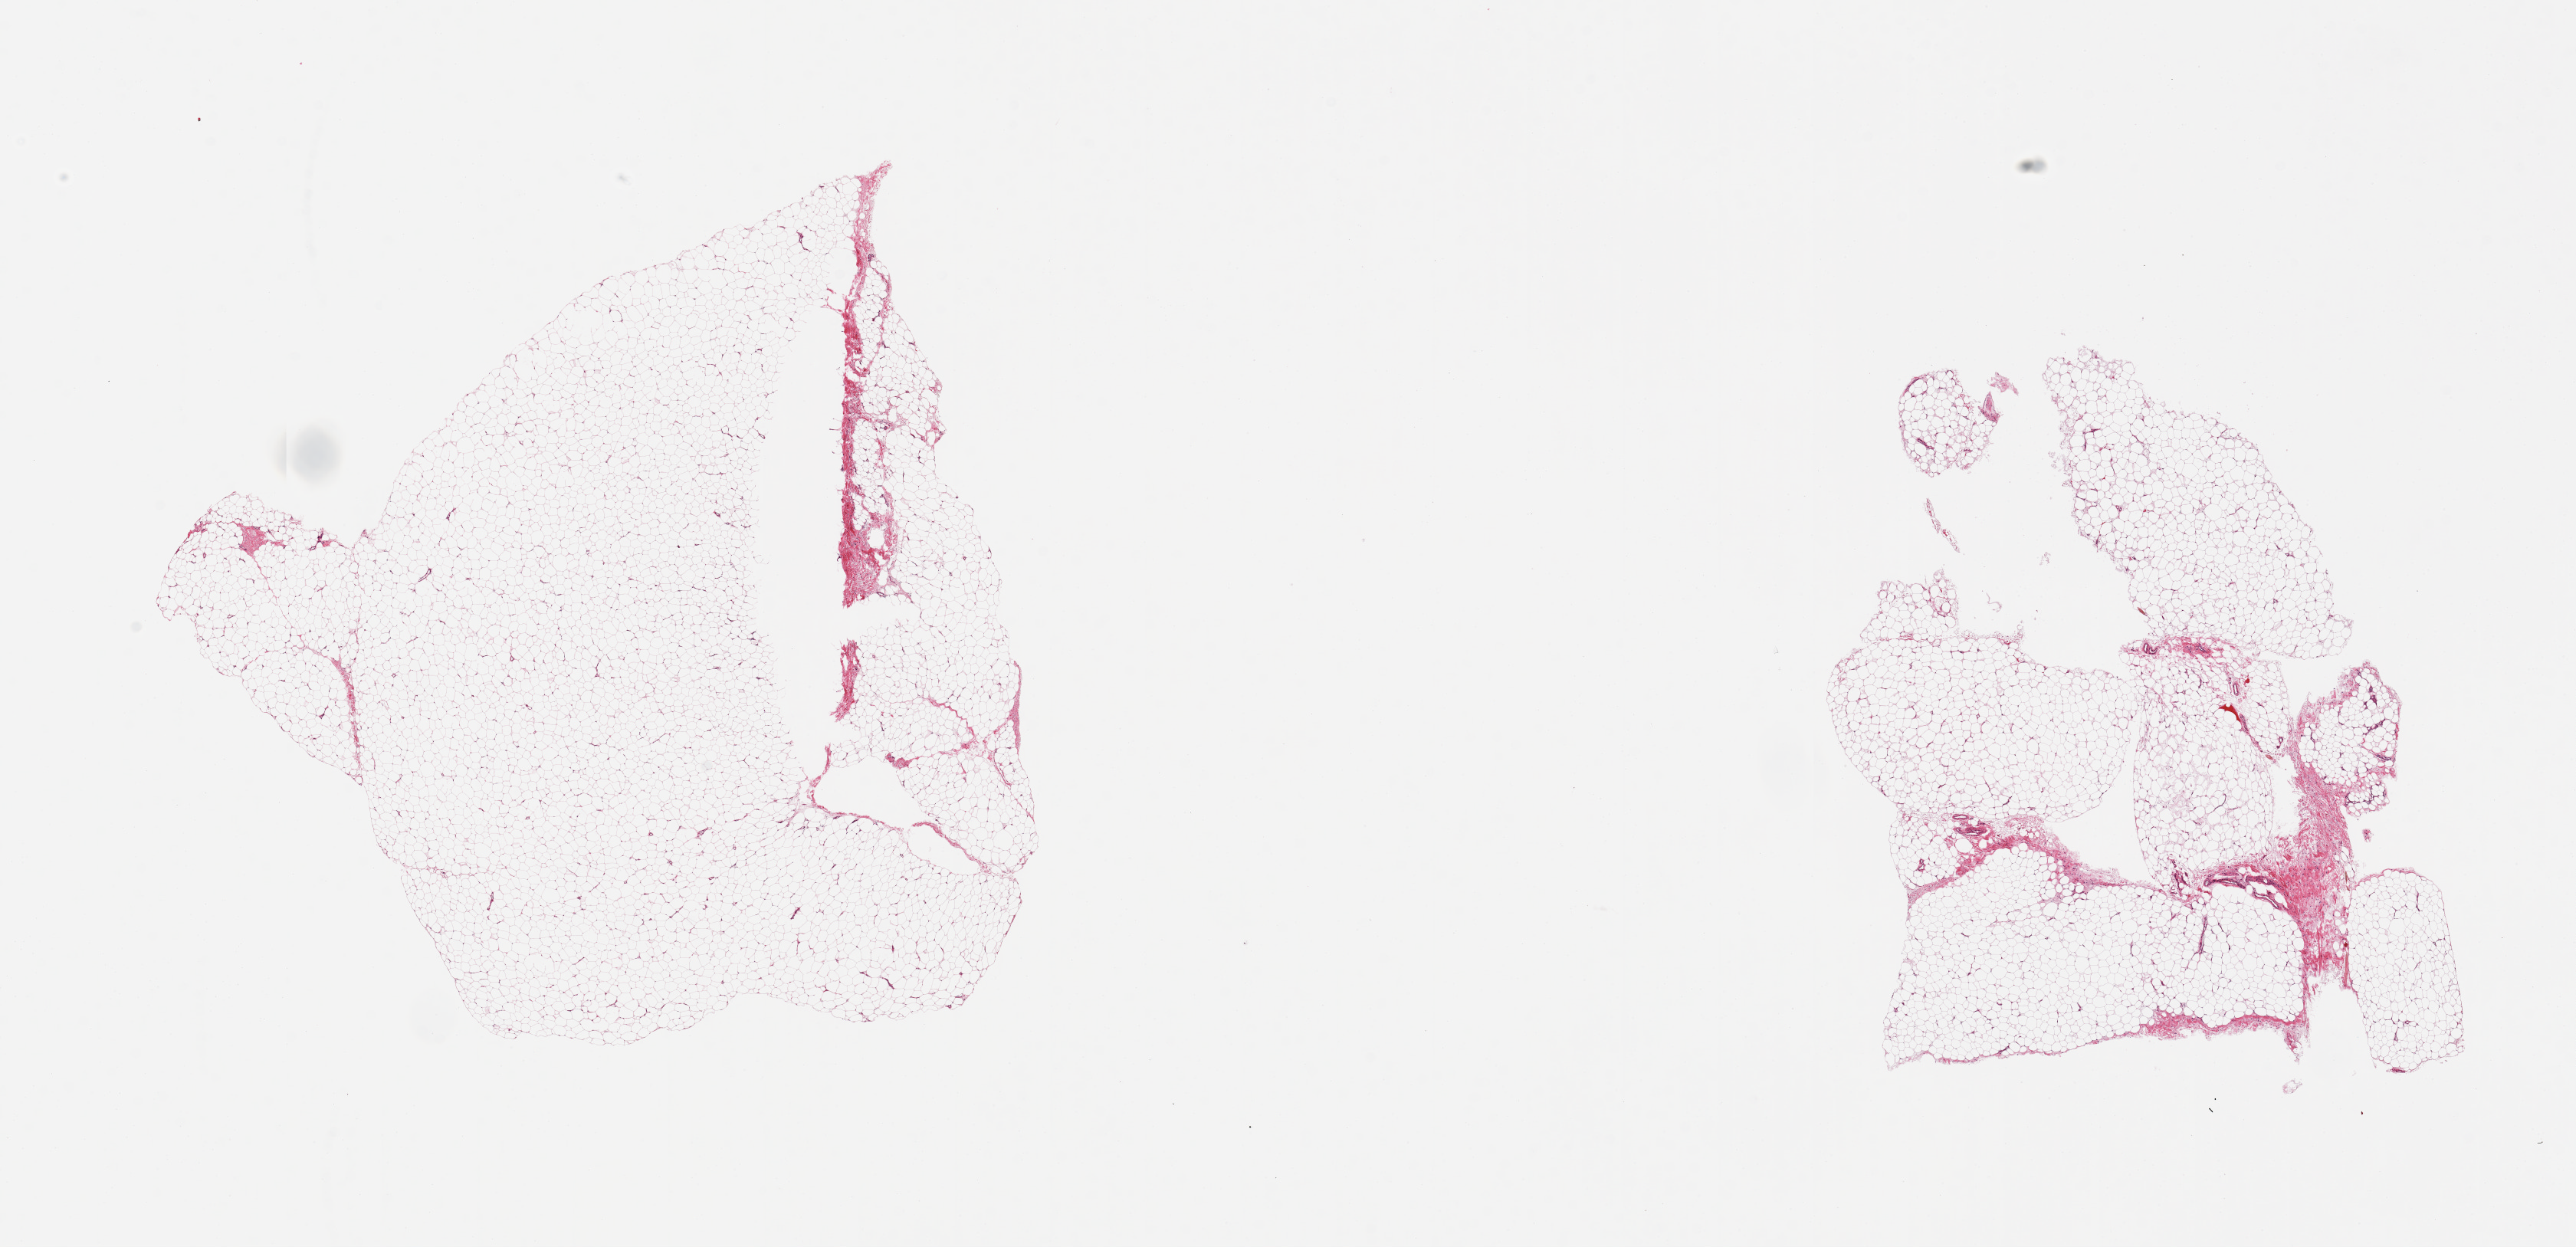
Haematoxylin and eosin whole-slide image, brightfield — whole scanned area (about 26.6 x 12.9 mm) shown as a low-resolution overview; PAXgene-fixed paraffin-embedded (PFPE) section; section of adipose tissue (target tissue); tissue donor sample. Male donor.
Reviewer comment on this tissue sample: 2 pieces.